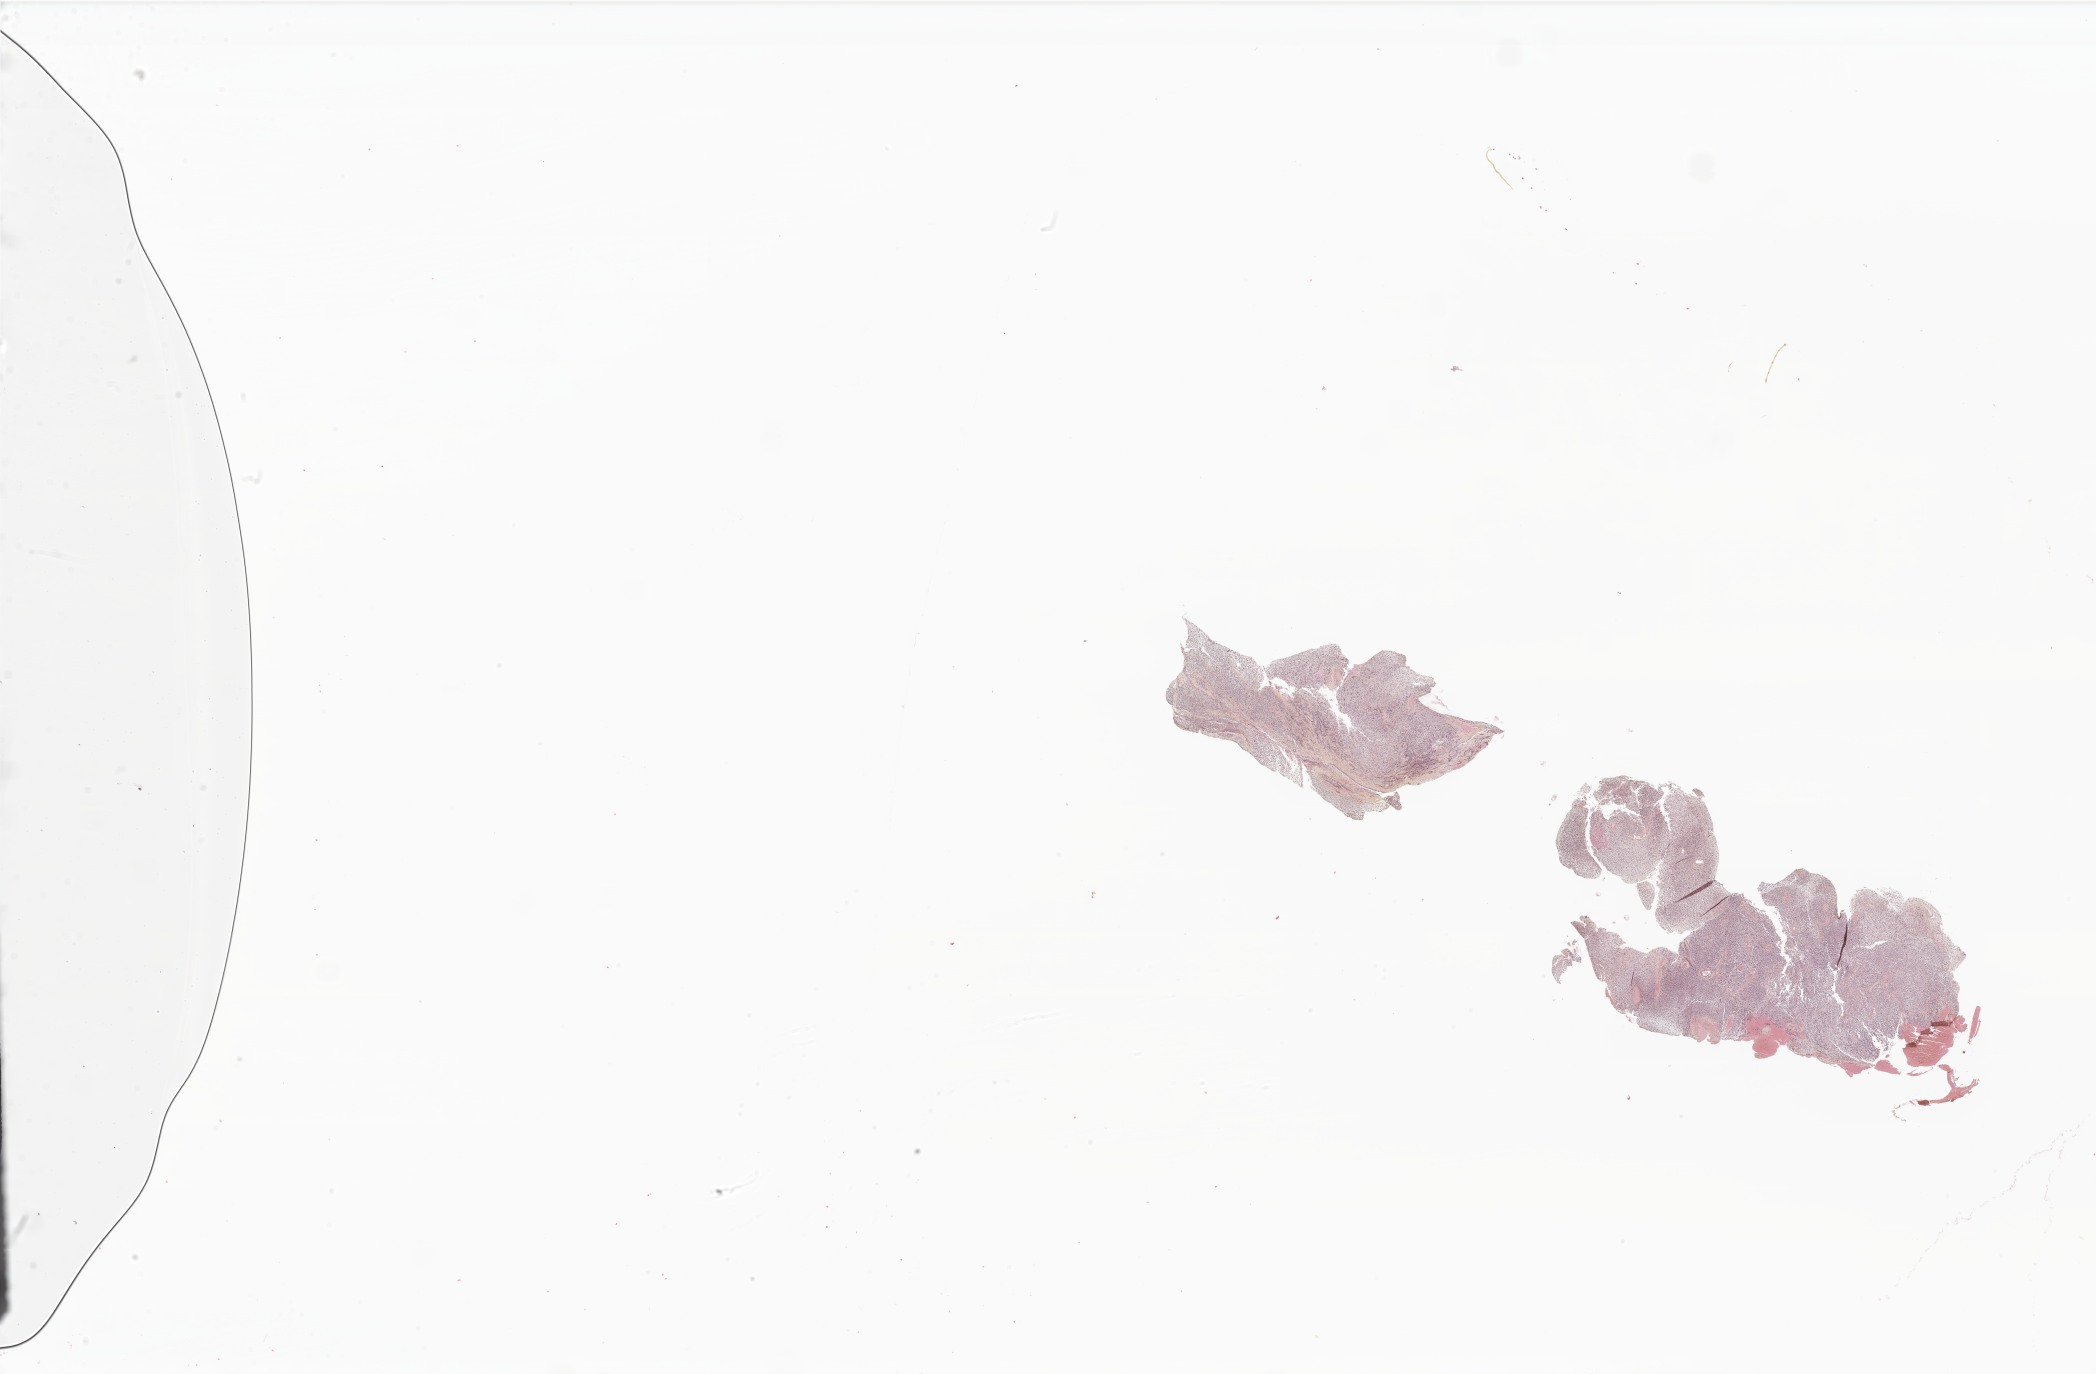
Whole-slide image, H&E stain of tumor tissue from the anterior wall of nasopharynx — whole scanned area (about 35.4 x 23.2 mm) shown as a low-resolution overview, formalin-fixed paraffin-embedded section. Male patient, age 123 months (10 years 3 months).
Diagnosis (ICD-O-3 morphology term): Embryonal rhabdomyosarcoma, NOS.